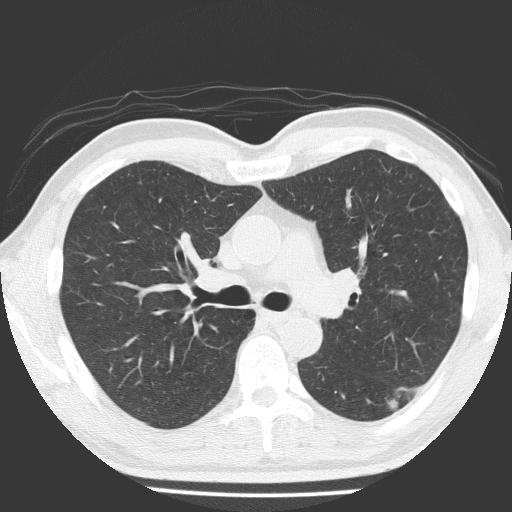
Low-dose screening chest CT, one axial slice. Reconstruction kernel FC51. Lung window (W 1500 / L -600 HU). 2 mm slice thickness. 512 × 512 image matrix, field of view 348 × 348 mm.
Annotated regions visible in this slice (manually delineated by an expert):
- lesion 1 (tumor, lower lobe of left lung): bounding box [x1, y1, x2, y2] px = [387, 395, 400, 412]